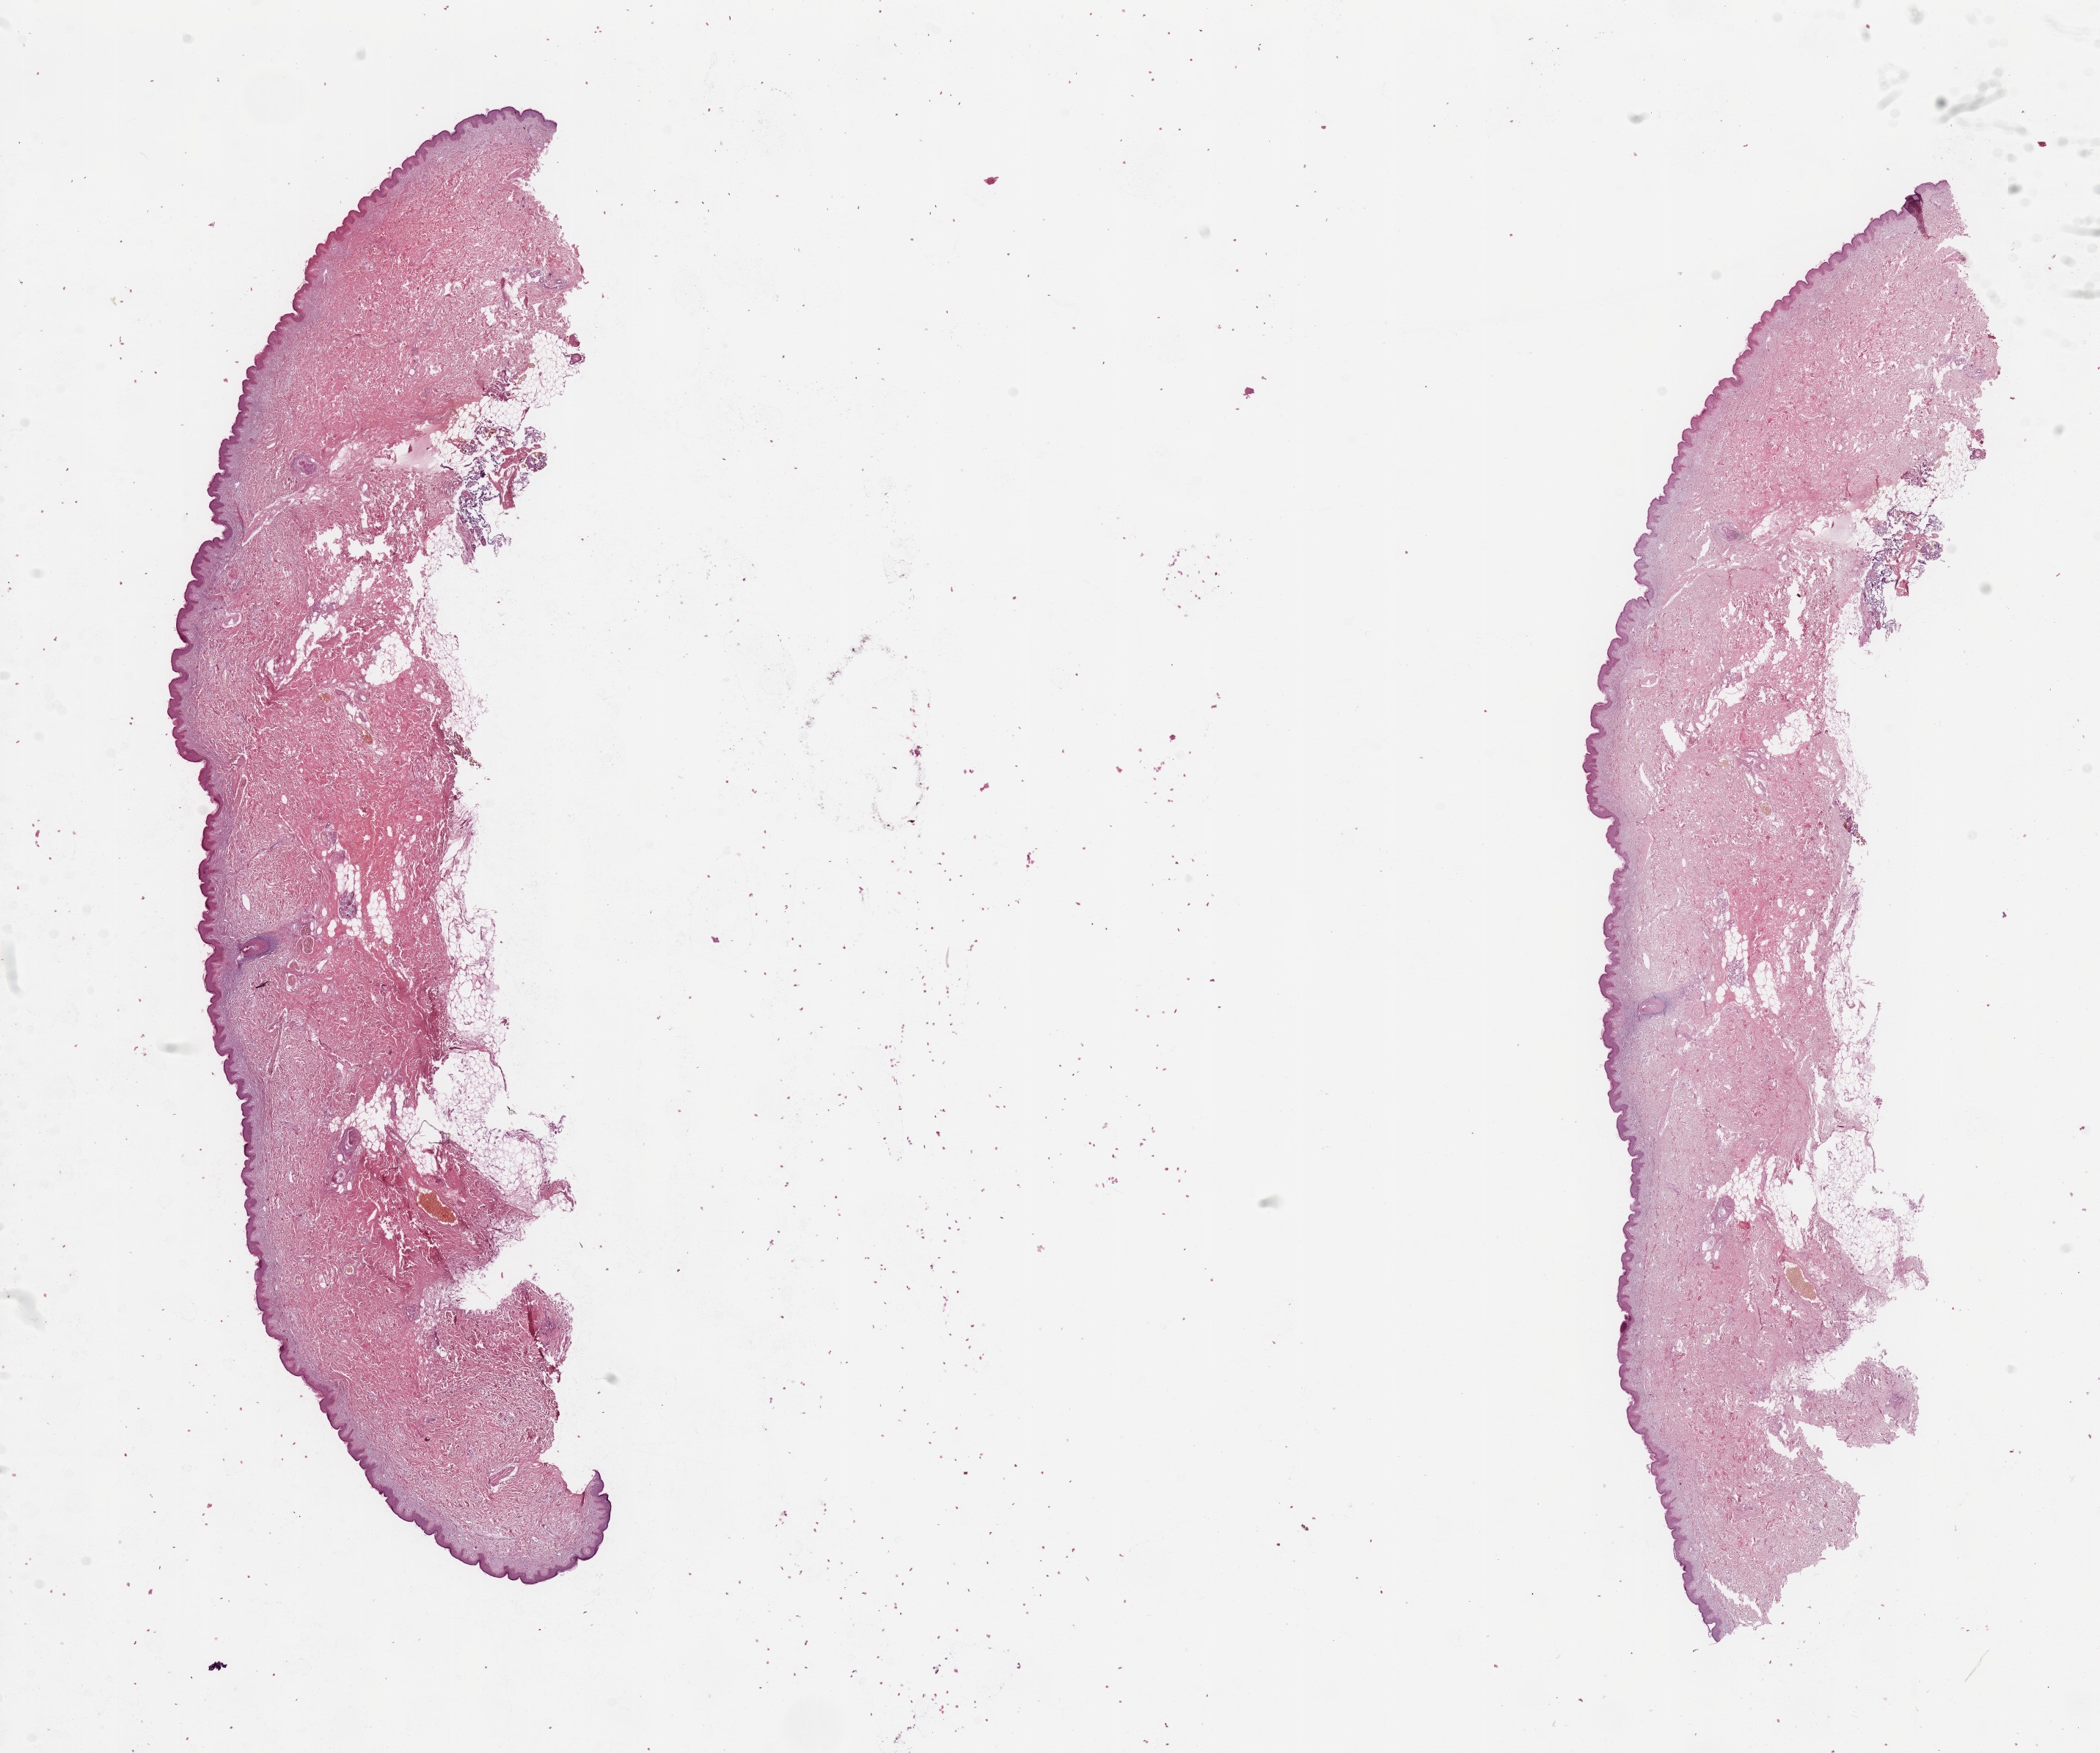
Digitized Hematoxylin and eosin (H&E) stained tissue section (whole slide), a low-resolution overview of the entire scanned area, about 22.6 x 18.9 mm (acquisition: 20x scan); normal (non-tumour) tissue sample. Patient: female, age 50 years.
* this section: normal (non-tumour) tissue from the same patient
* patient diagnosis (cohort enrolment): sarcoma (site not recorded at cohort level)